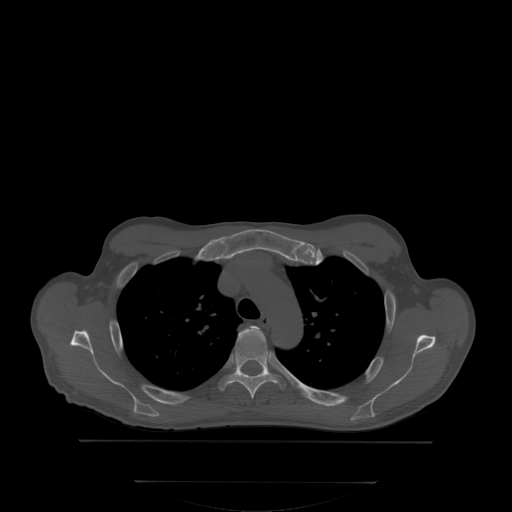
CT including the spine, one axial slice; position 259 of 350 along the scan axis; bone window (W 1800 / L 400 HU); 512 × 512 image matrix. Male patient, age 58 years. From the clinical record (not read from this slice): primary cancer: prostate.
Structures marked on this image (semi-automatically segmented with operator editing):
- T3 vertebra: bounding box (x1, y1, x2, y2) in pixels: (247, 327, 260, 333)
- T4 vertebra: (218, 330, 286, 397)